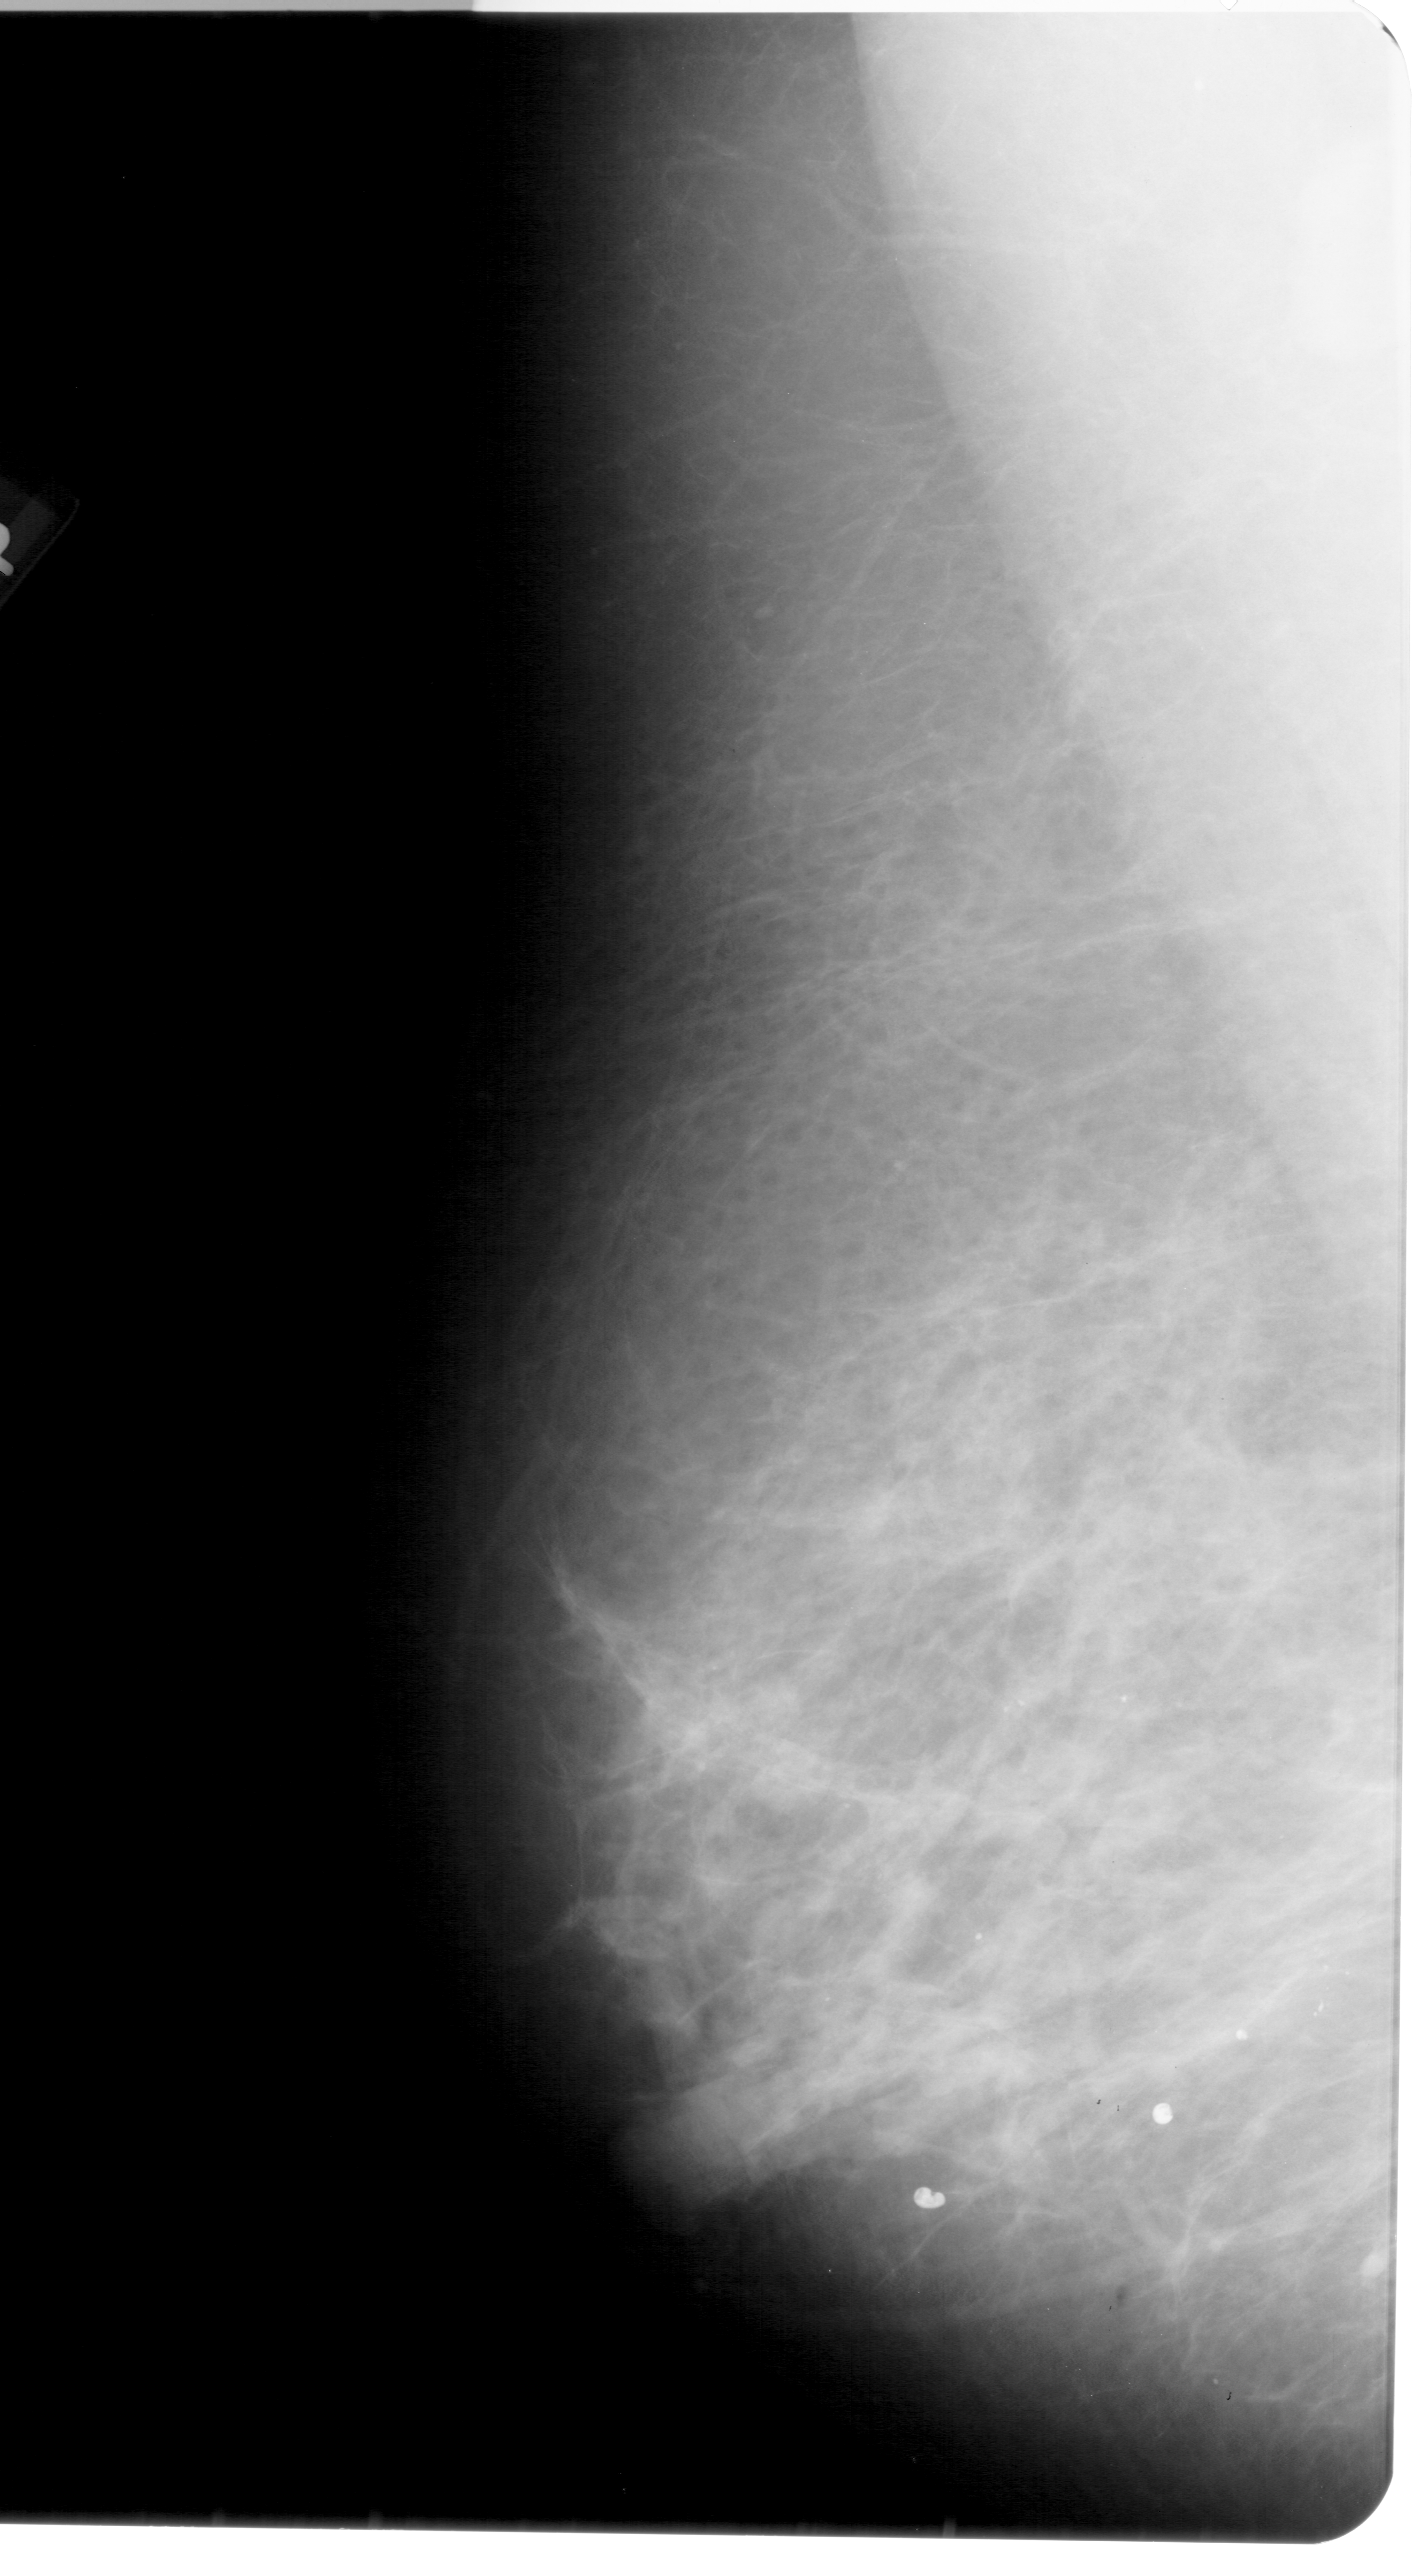
Mammogram (digitized film); left breast; mediolateral oblique (MLO) view; breast composition: scattered fibroglandular densities (BI-RADS density category 2 of 4).
- Calcifications, morphology pleomorphic, distribution clustered; BI-RADS assessment category 4; pathology (as recorded): benign.